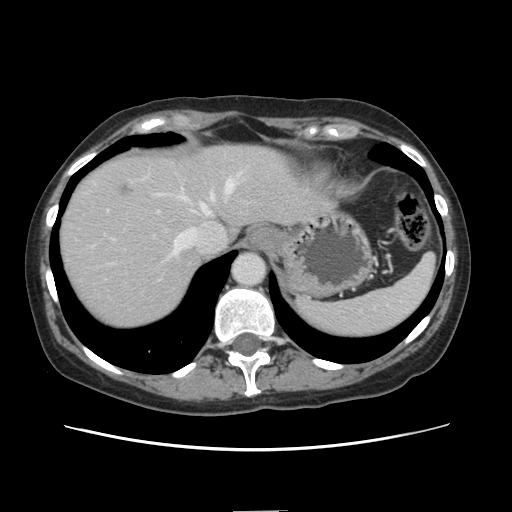
Contrast-enhanced abdominal CT, one axial slice. Slice 116 of 141 in the series (ordered by position). 120 kVp. Soft-tissue window (W 400 / L 40 HU). 2.5 mm slice thickness. 512 × 512 image matrix, field of view 350 × 350 mm. Female patient, age 63 years. From the clinical record (not read from this slice): diagnosis: colorectal cancer liver metastases, imaged before liver resection; multiple liver metastases: yes; largest metastasis: 3.2 cm; disease in both lobes: yes.
Annotated regions visible in this slice (expert manual segmentation):
- hepatic veins: bounding box [x1, y1, x2, y2] px = [165, 180, 234, 261]
- liver: [59, 144, 330, 330]
- planned liver remnant (the part of the liver to remain after resection): [199, 145, 329, 234]
- portal vein (with intrahepatic branches): [159, 183, 235, 211]